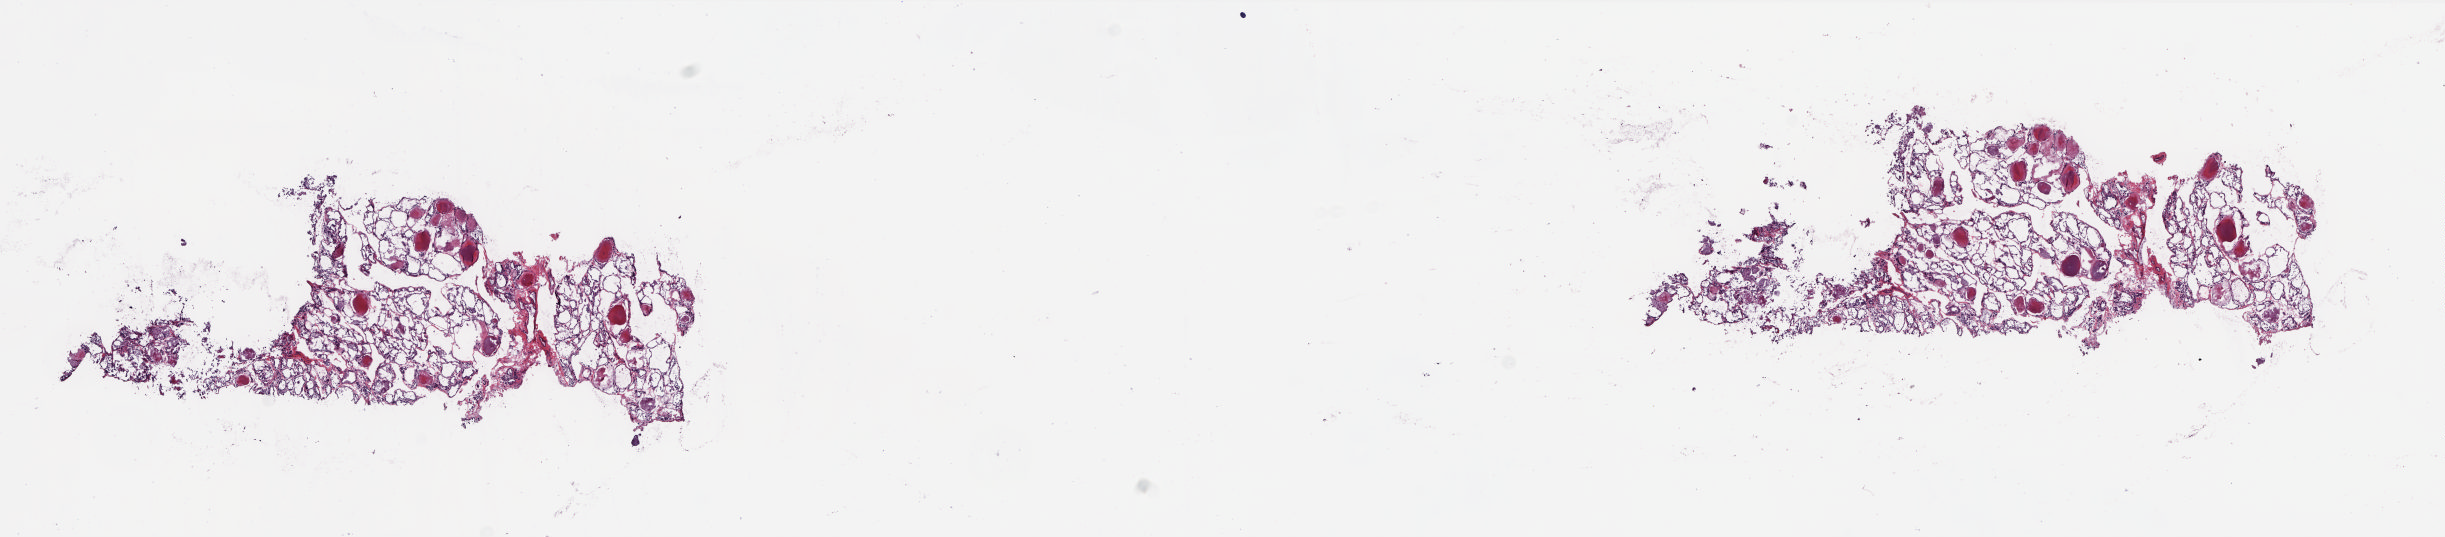
Whole-slide histology image, Hematoxylin and eosin (H&E) stained, low-resolution overview of the scanned area, about 19.7 x 4.3 mm (from a 20x scan), frozen section from the top of the tissue portion, thyroid, solid tissue normal (non-tumour tissue) sample. Female, age 54 years at initial diagnosis. Pathologist review of this section (percent, as recorded): tumour cells 0%, tumour nuclei 0%, normal cells 100%, stromal cells 0%, necrosis 0%. Infiltration values recorded for this section: lymphocyte infiltration 2%, monocyte infiltration 2%, neutrophil infiltration 0%.
* this section: solid tissue normal sample (biorepository sample class)
* patient diagnosis: Papillary adenocarcinoma, NOS (thyroid gland)